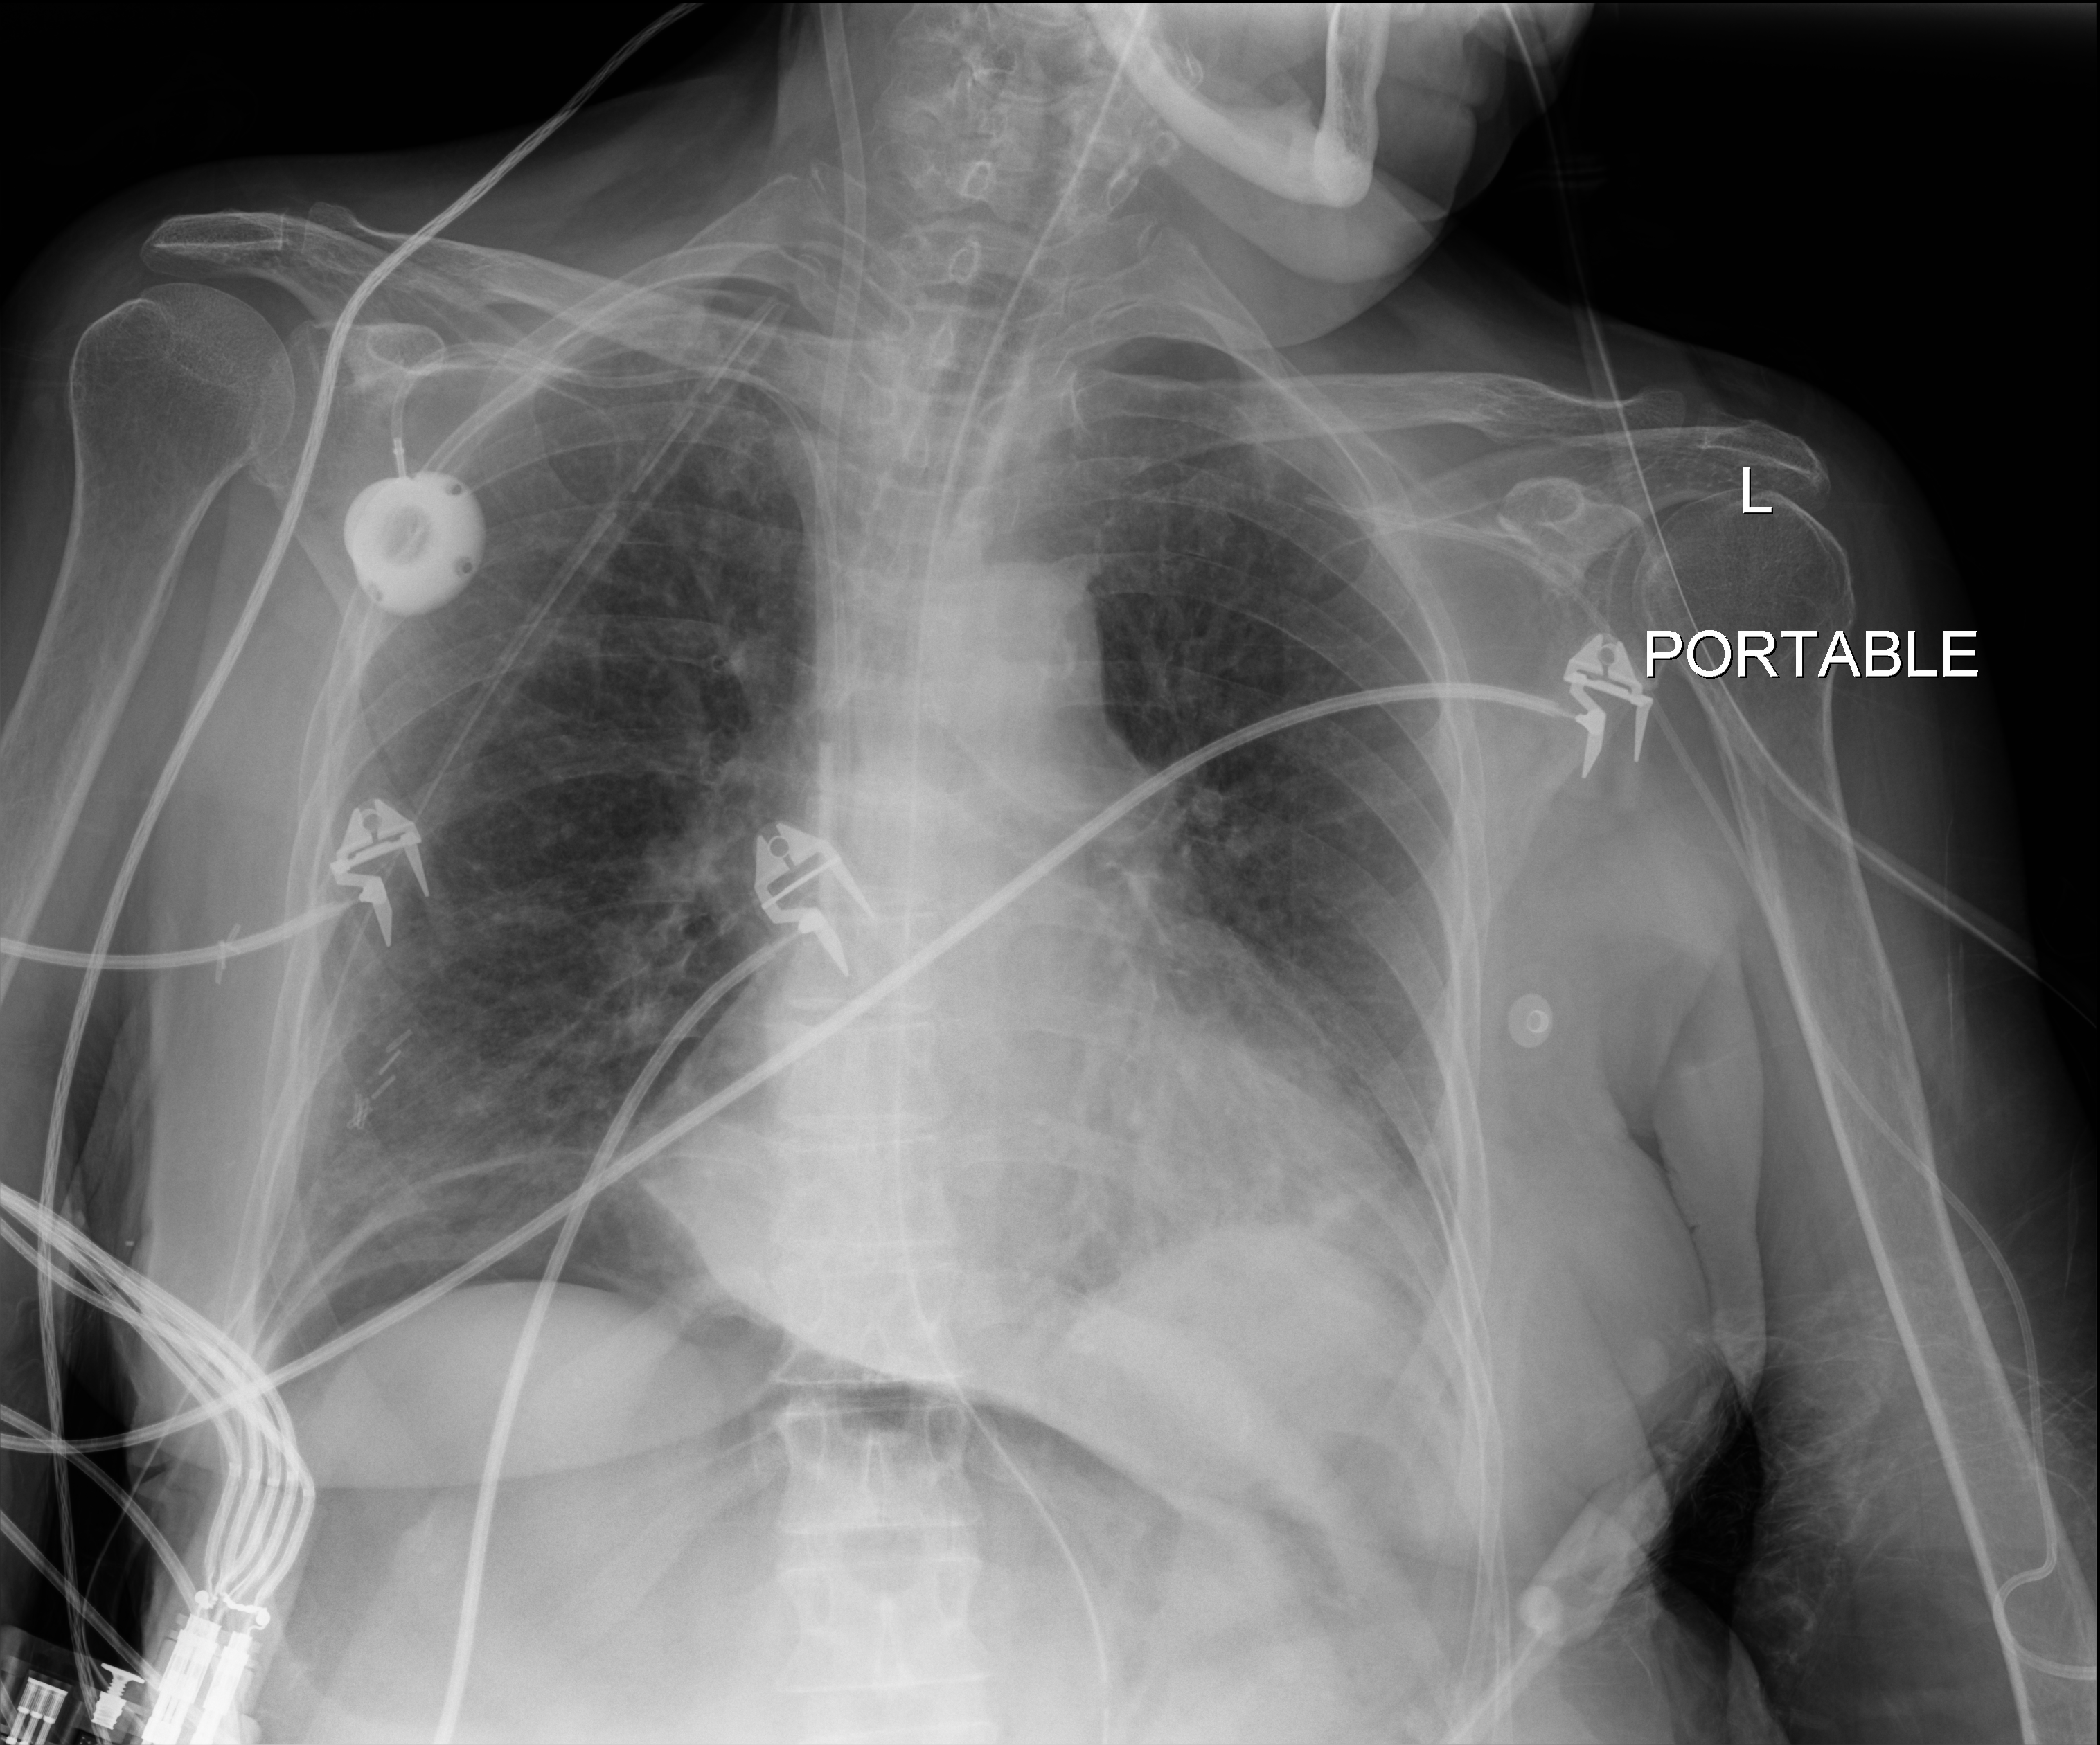
Chest X-ray (portable), anteroposterior (AP) projection. Female patient hospitalised with COVID-19, age 60–74 years.
Hospital-stay facts (about this admission, not read from this image; timing relative to this image not recorded): COPD (admission record): no; hypertension (admission record): yes.